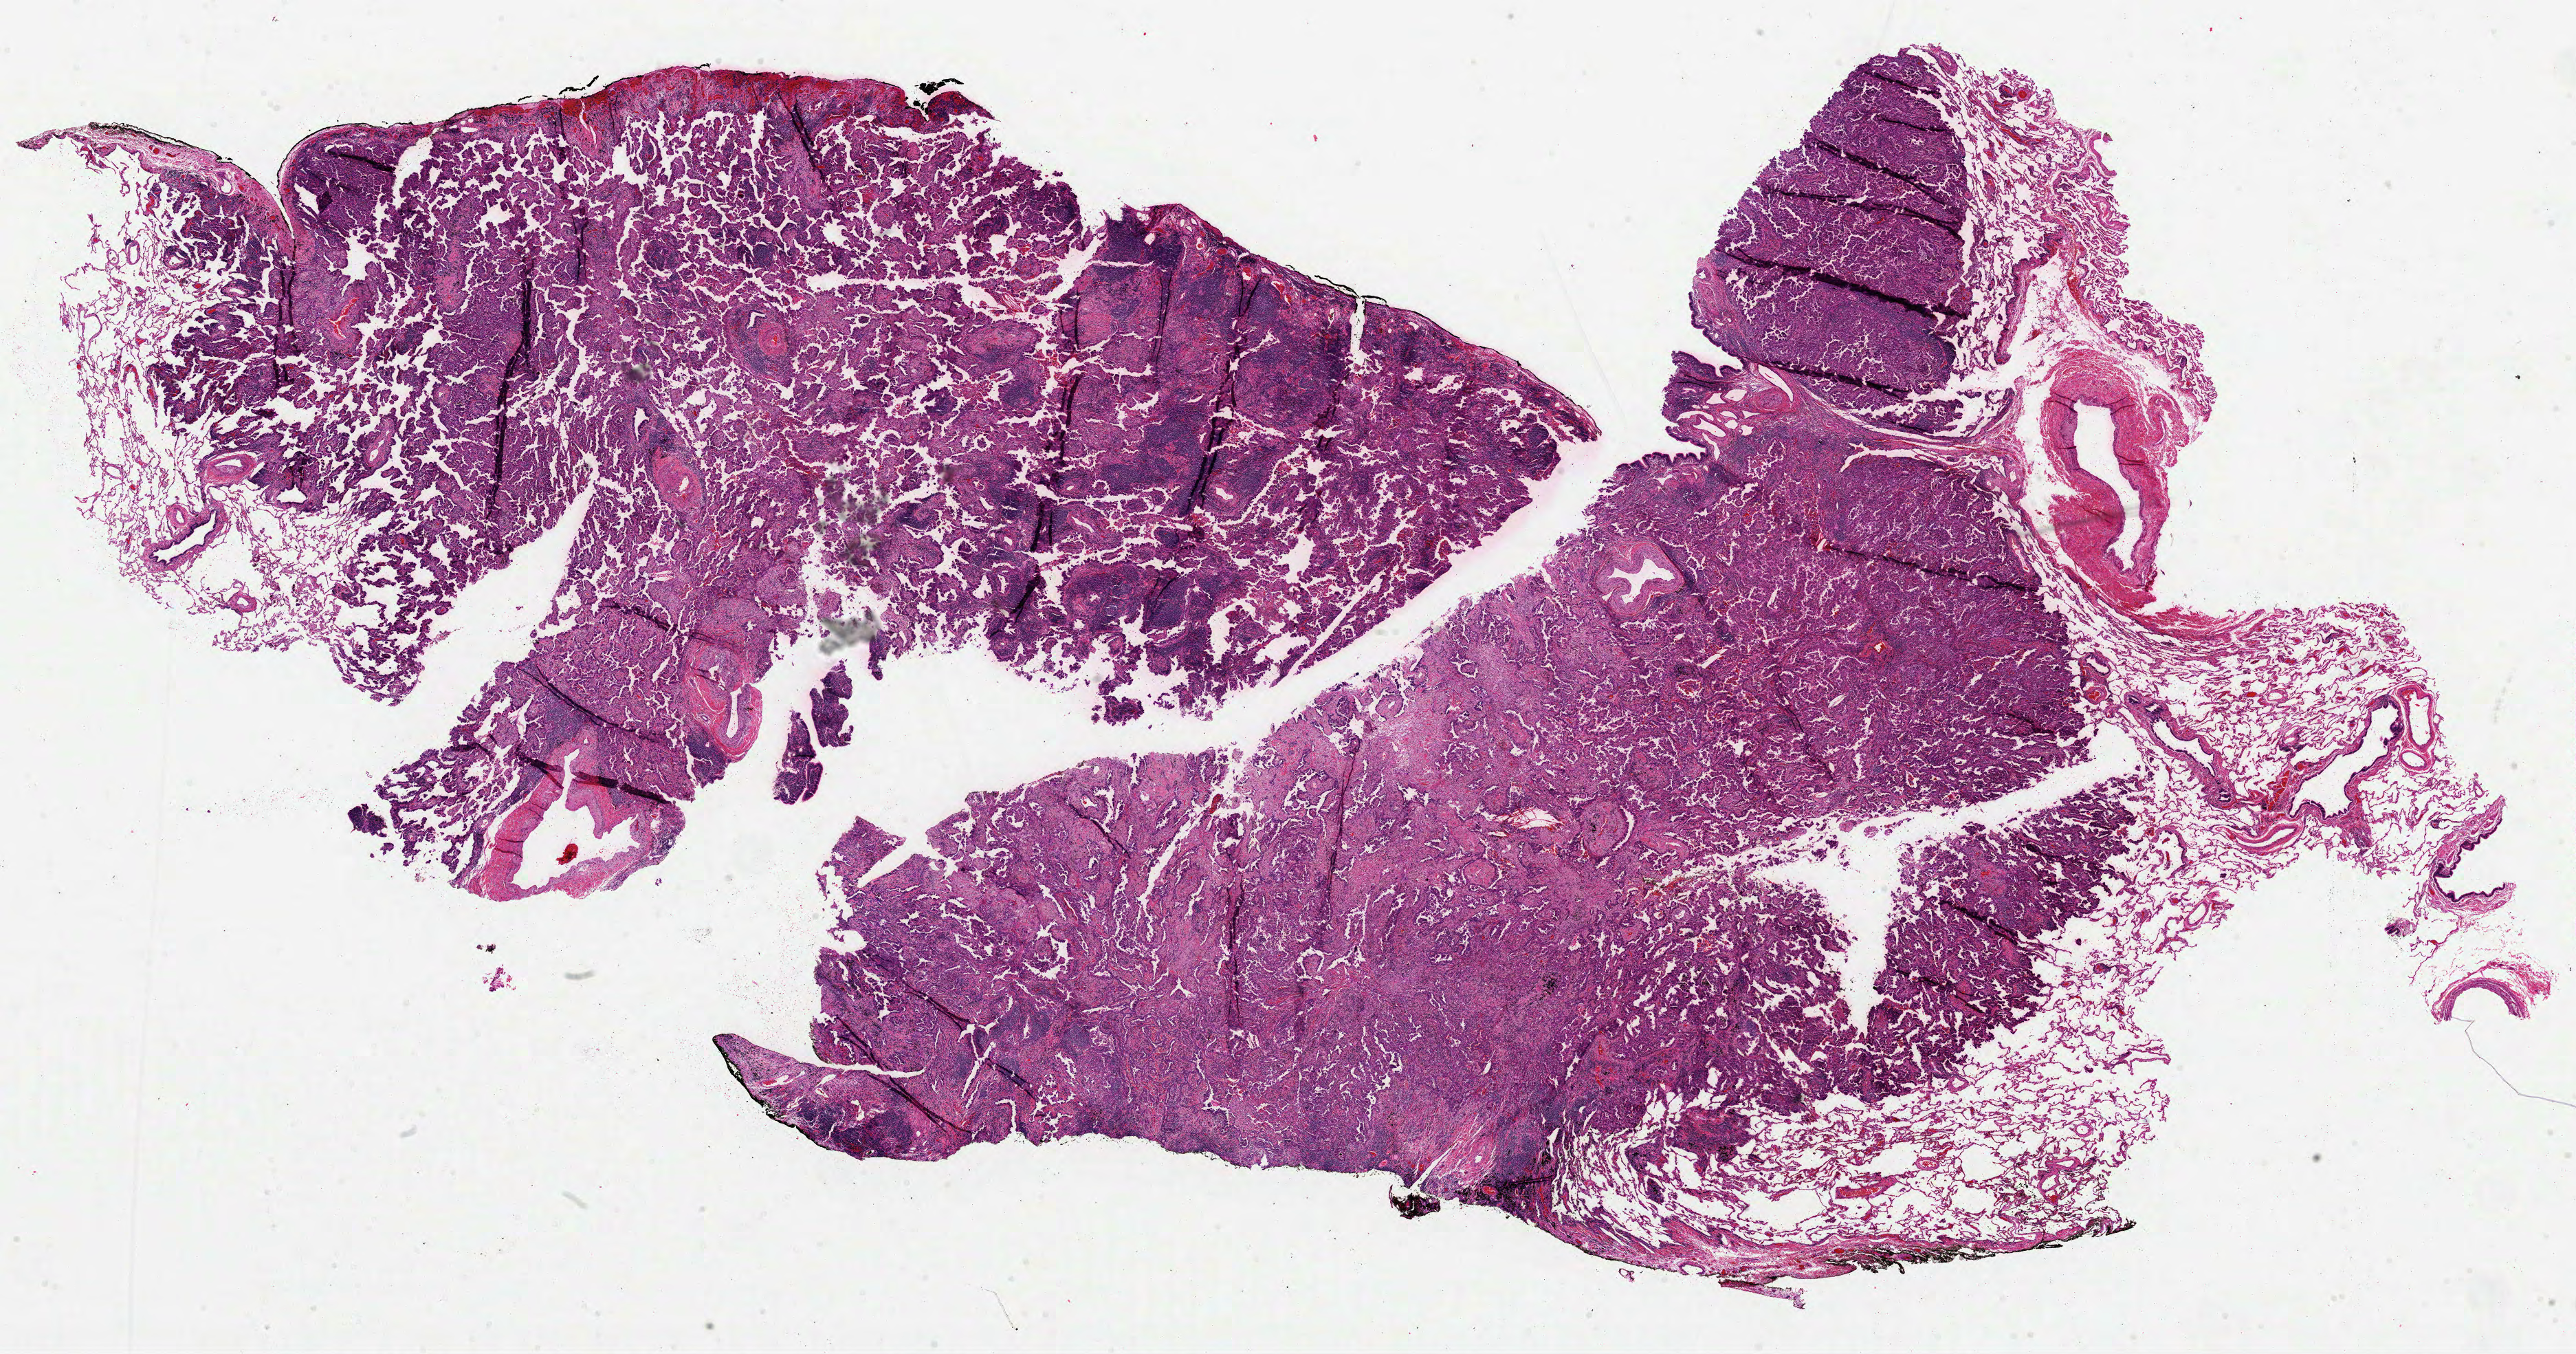
H&E-stained whole-slide image — shown as a low-resolution overview of the whole scanned area (about 30.2 x 15.9 mm, slide scanned at 40x), formalin-fixed paraffin-embedded (FFPE) diagnostic section, primary tumour sample from the lung. Patient: female, age at initial diagnosis 74 years.
- diagnosis: Adenocarcinoma, NOS (lower lobe, lung)
- AJCC pathologic stage: IA (3rd edition)